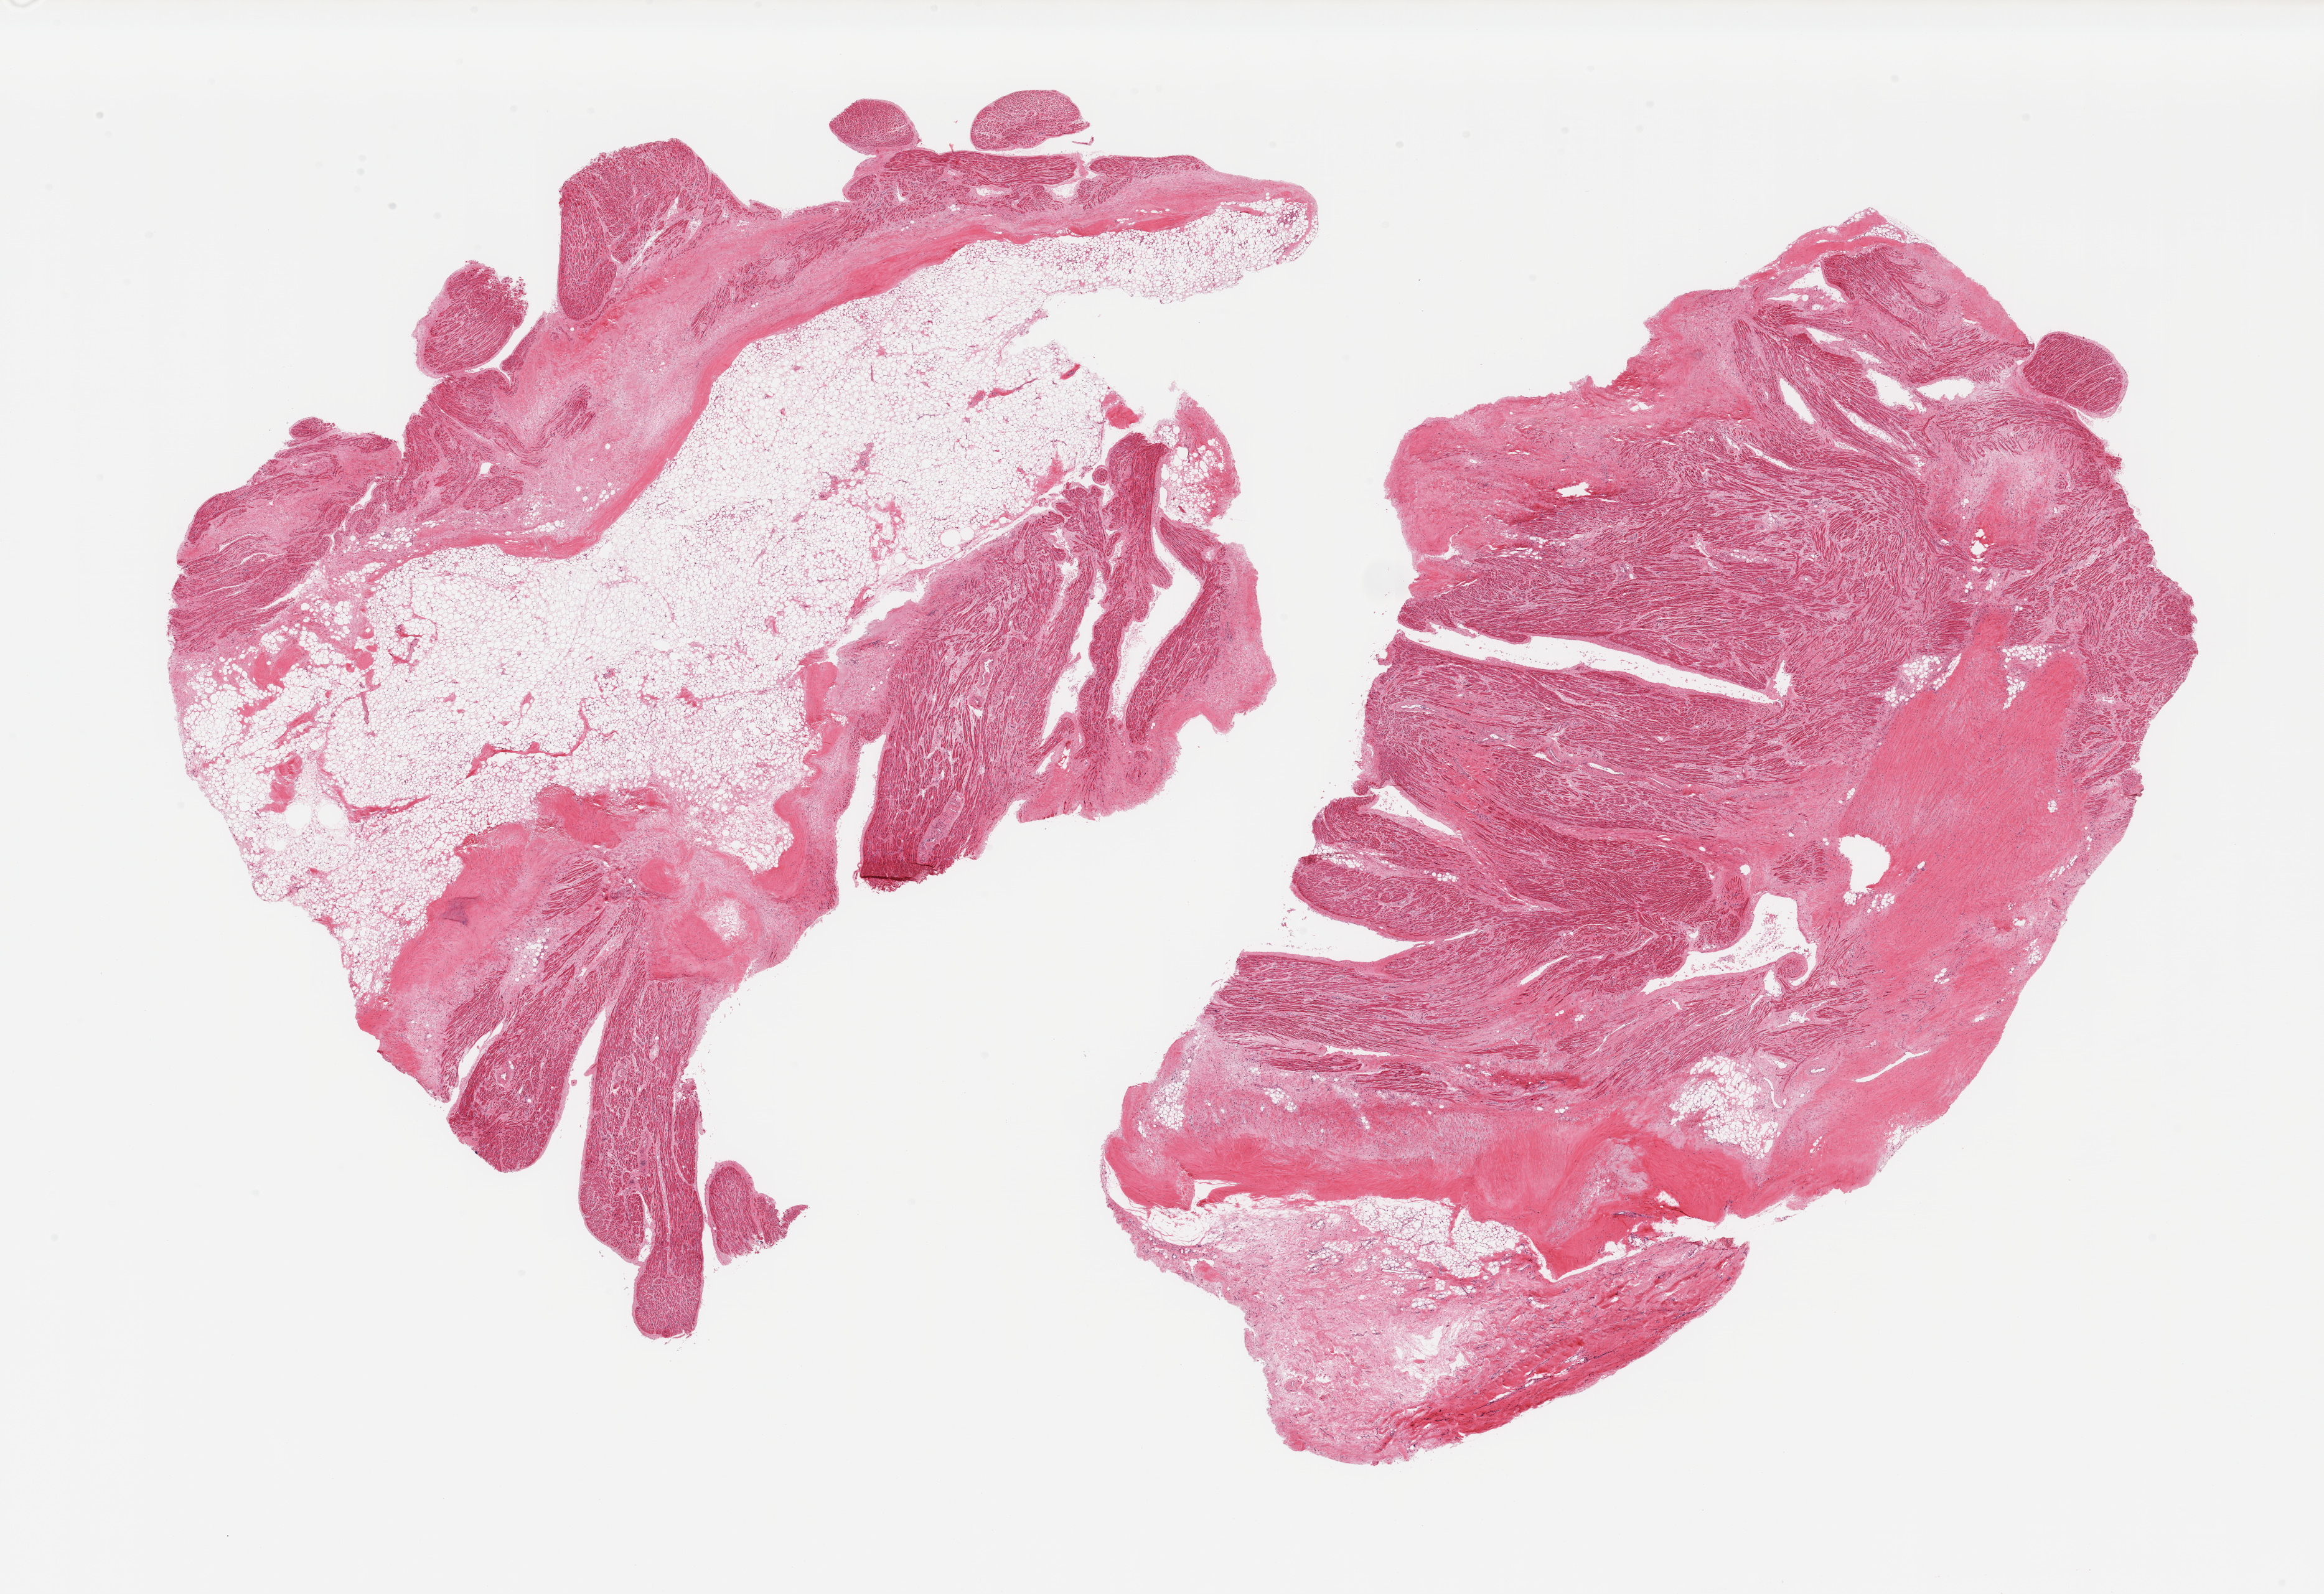
Digitized H&E-stained section, whole scanned area (about 29.5 x 20.3 mm) shown as a low-resolution overview, PAXgene-fixed, paraffin-embedded tissue, sampled site (target tissue): auricular appendage, tissue donor sample. Donor: male.
Pathologist's review note for this sample: 2 pieces; ~70% and 40% internal fibrous tissue and fat.